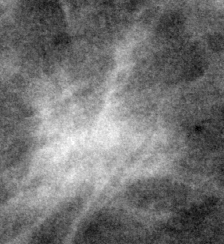
Region of interest cut from a scanned film mammogram (one marked finding); right breast; MLO view.
- Mass, shape irregular, margins spiculated; BI-RADS assessment category 4; pathology result (as recorded, not read from the image): benign.